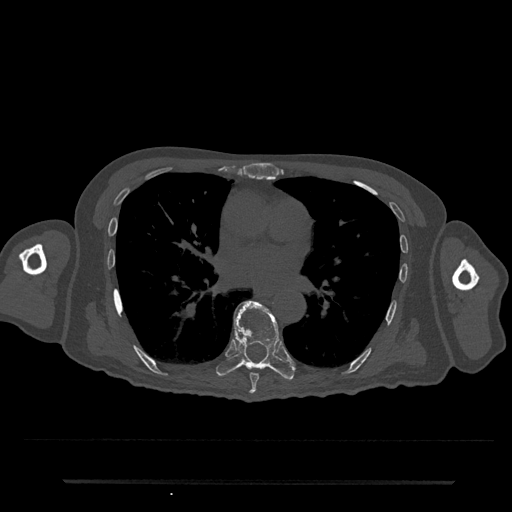
CT including the spine, one axial slice. Slice 442 of 797 in the series (ordered by position). Reconstruction kernel Br40s/3. Bone window (W 1800 / L 400 HU). 0.5 mm slice thickness. 512 × 512 image matrix, field of view 427 × 427 mm. Patient: male, 74 years. From the clinical record (not read from this slice): primary cancer: prostate.
Annotated regions visible in this slice (semi-automatic segmentation, software-assisted and operator-edited):
- T7 vertebra: bounding box <249,373,259,394> (left, top, right, bottom; pixels)
- T8 vertebra: <216,301,295,380>